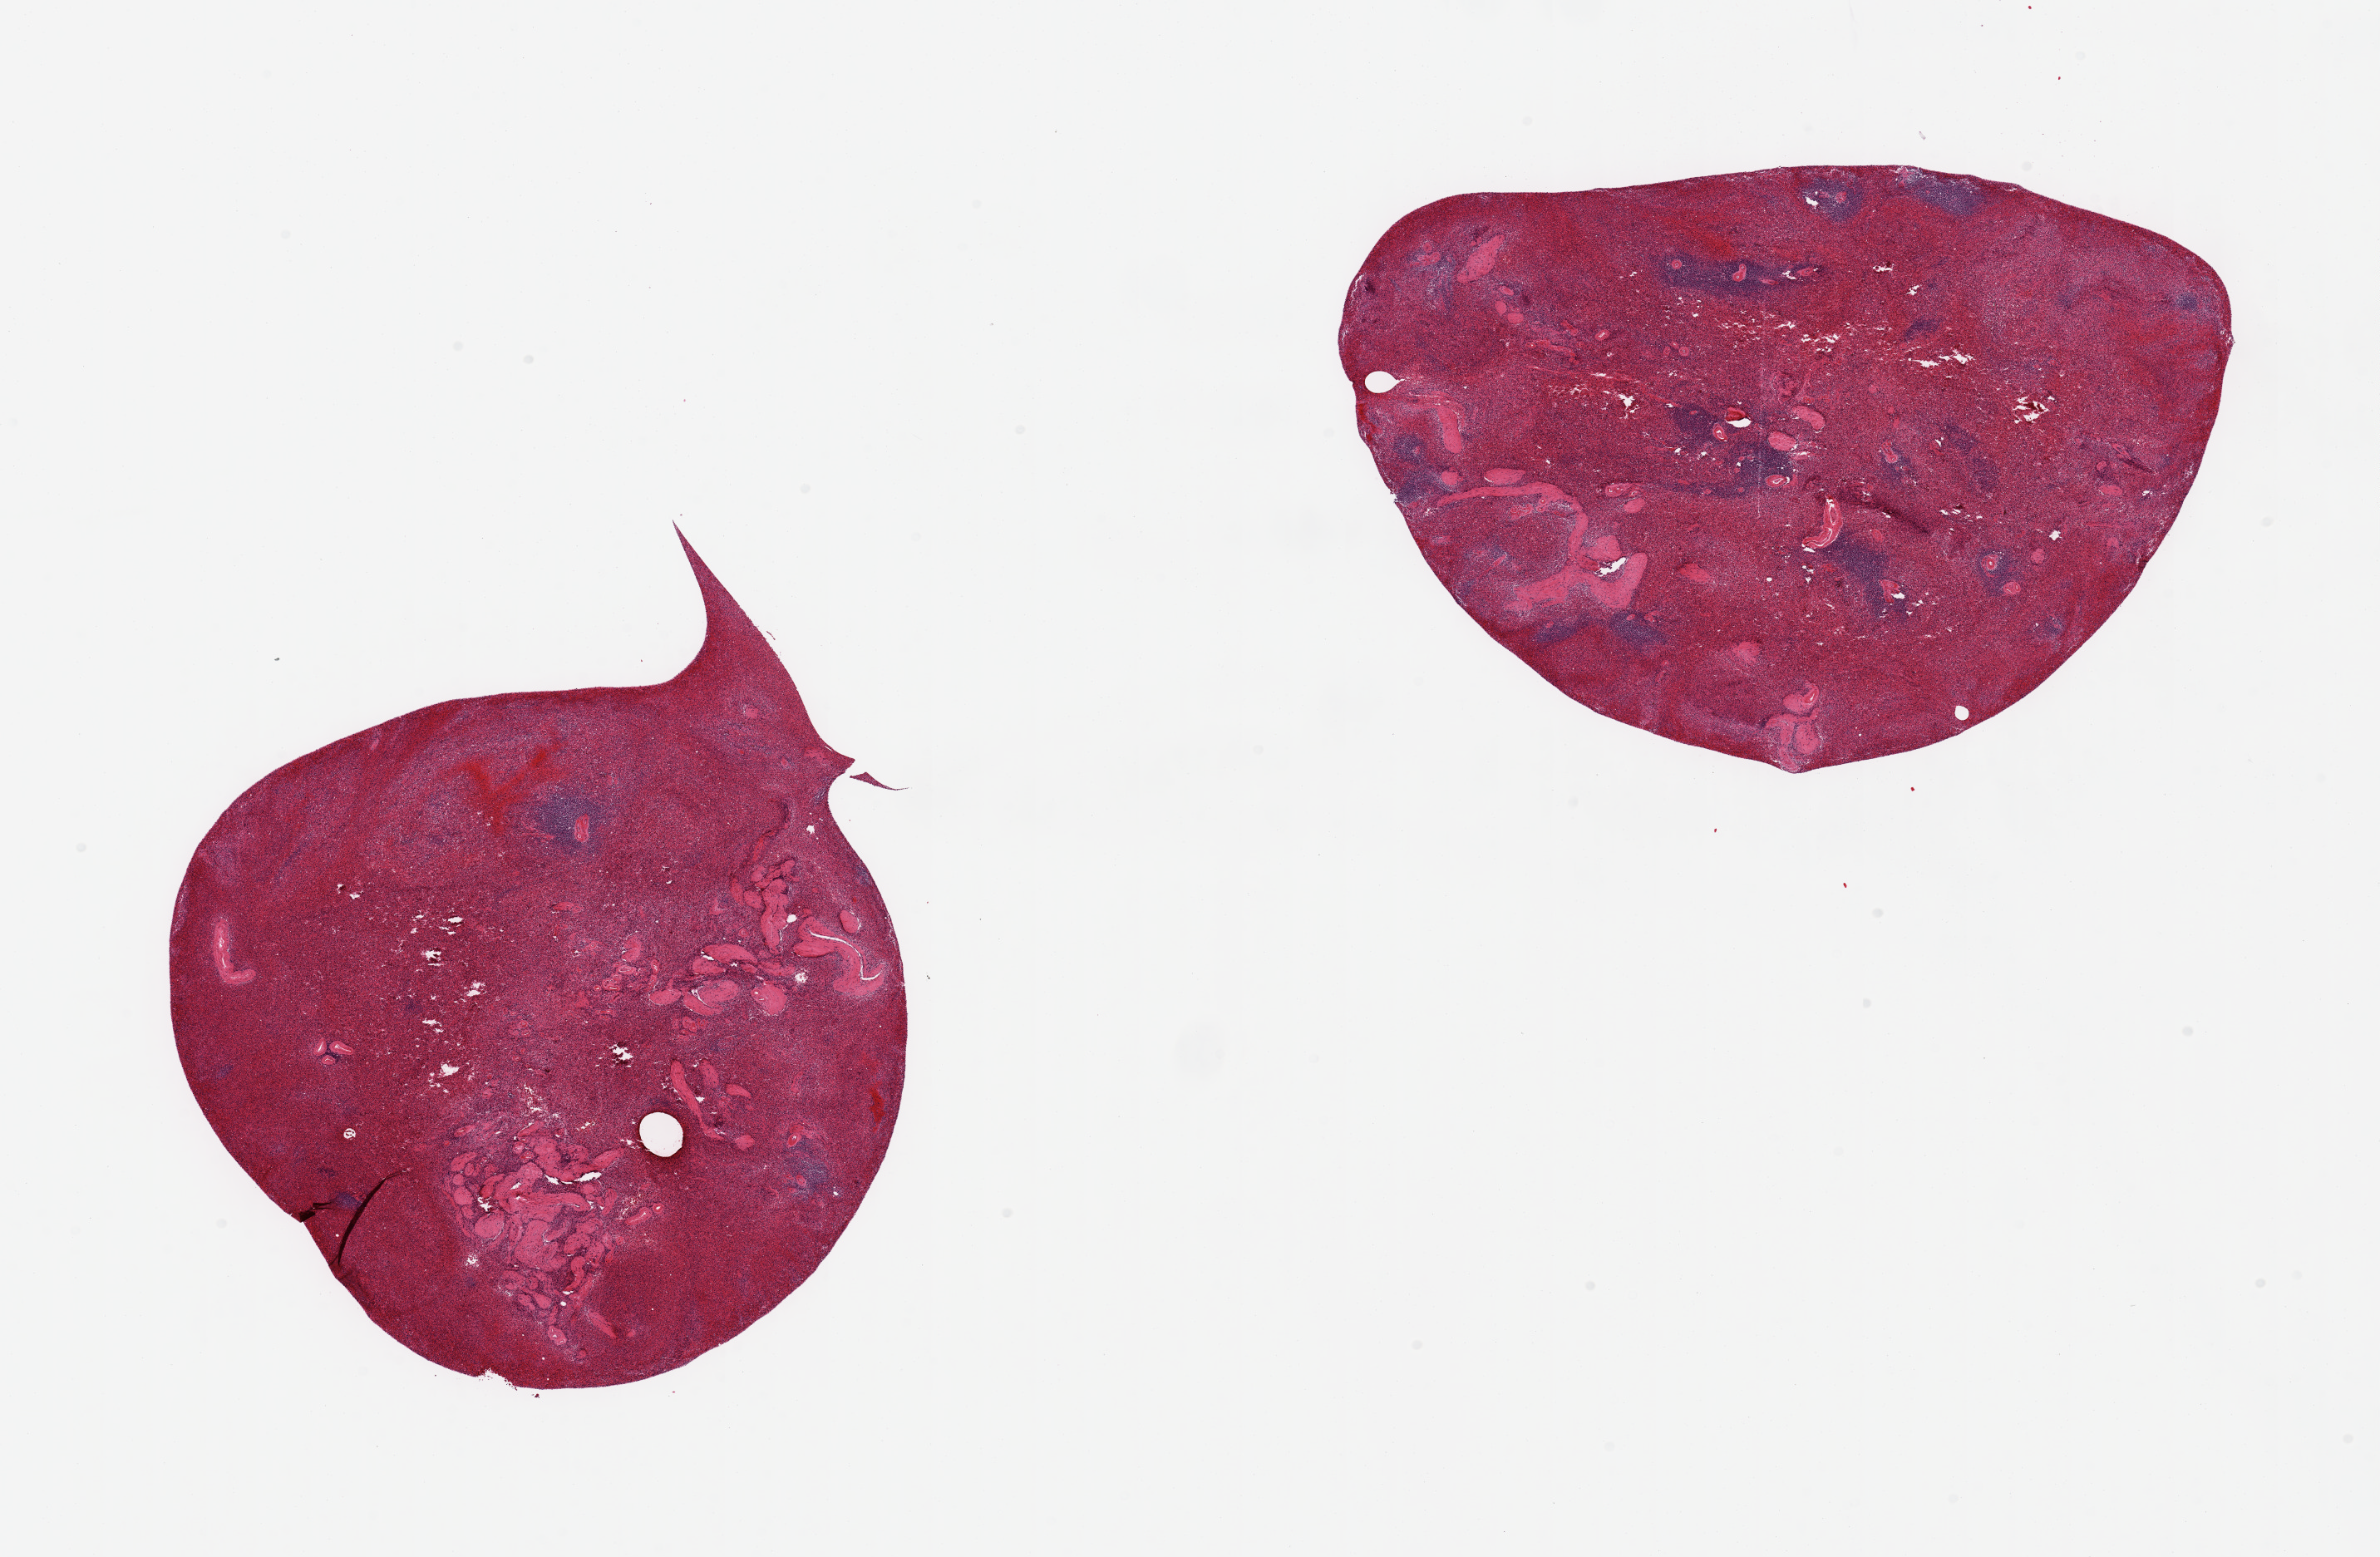
Haematoxylin and eosin whole-slide image, low-resolution overview of the scanned area, about 22.6 x 14.8 mm, PAXgene-fixed paraffin-embedded (PFPE) section, target tissue: spleen, donor tissue sample. Donor: female.
Pathologist's review note for this sample: 2 pieces; moderate to severe vascular congestion.